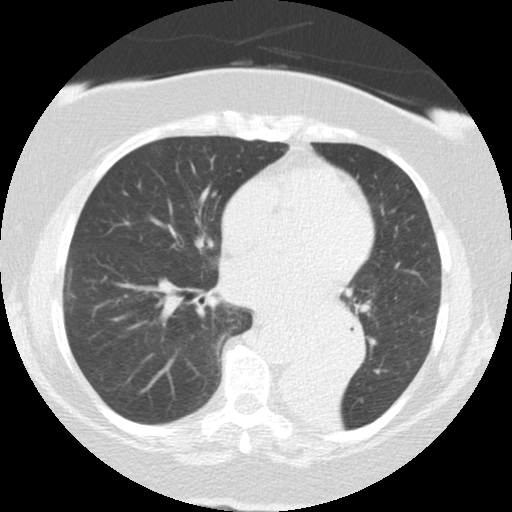
Low-dose screening chest CT, axial slice; baseline annual screen; lung window (W 1500 / L -600 HU); 2.5 mm slice thickness; slice 71 of 136 in the series. Female participant, aged 71 years at enrolment. Former smoker at enrolment.
- Expert-annotated lung lesion, bounding box [x1, y1, x2, y2] px = [283, 305, 367, 384].
- The exam's reader record, not a measurement of the box and not confirmed to be the same lesion: non-calcified nodule or mass ≥4 mm, right middle lobe, 5 × 5 mm, smooth margins, soft tissue attenuation.
- Note: the box lies in the patient's left hemithorax on this image, whereas the reader's record names the right lung; they may be different findings.
- Lung cancer was diagnosed 46 days after this screen: large cell carcinoma, NOS, left lower lobe, mediastinum, other location, poorly differentiated (G3), stage IV (AJCC 6th edition), 50 mm at pathology.